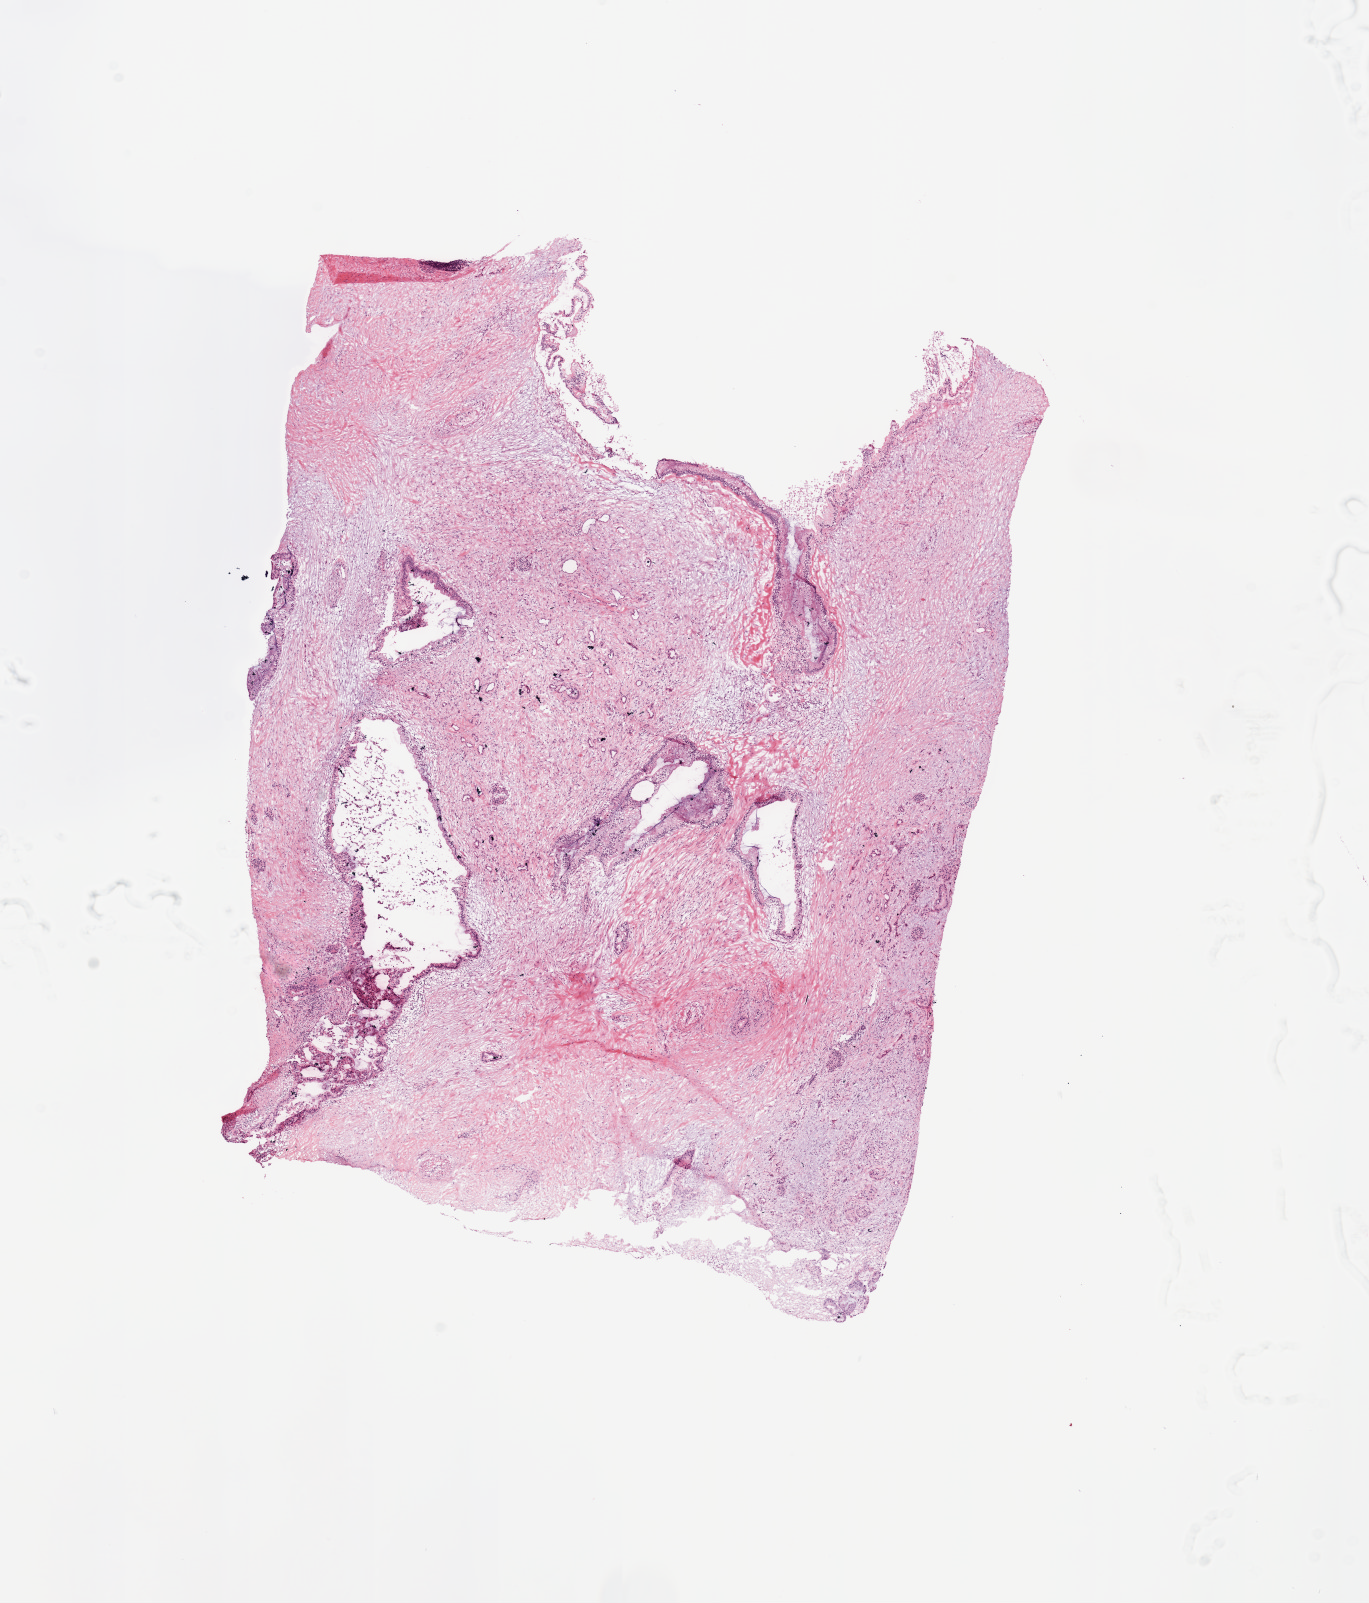
Whole-slide histology image, H&E-stained, whole scanned area (about 10.8 x 12.7 mm) shown as a low-resolution overview. Pancreas, tumour tissue. 69-year-old male patient.
Diagnosis: Infiltrating duct carcinoma, NOS.